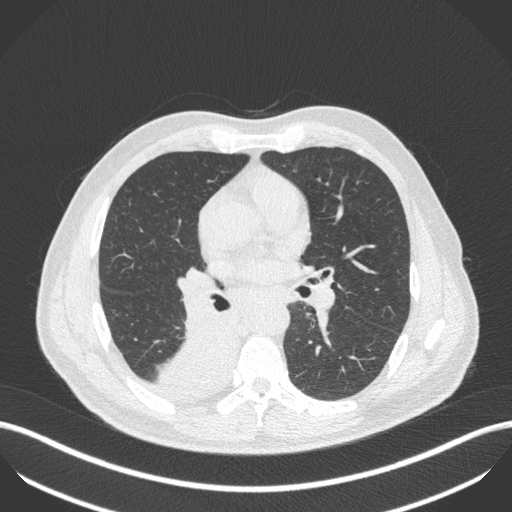
Chest CT, one axial slice; position 256 of 451 along the scan axis; reconstruction kernel B31f; 100 kVp; lung window (W 1500 / L -600 HU); 1 mm slice thickness; 512 × 512 image matrix. Male patient, age 61 years. Case-level facts recorded for this patient, not image findings: clinical TNM (as recorded): T1 N0 M0; histopathological grade: G3.
Annotated regions visible in this slice (bounding box drawn by a radiologist):
- lung tumour (recorded histology: small cell carcinoma): bounding box [x1, y1, x2, y2] px = [156, 316, 251, 400]